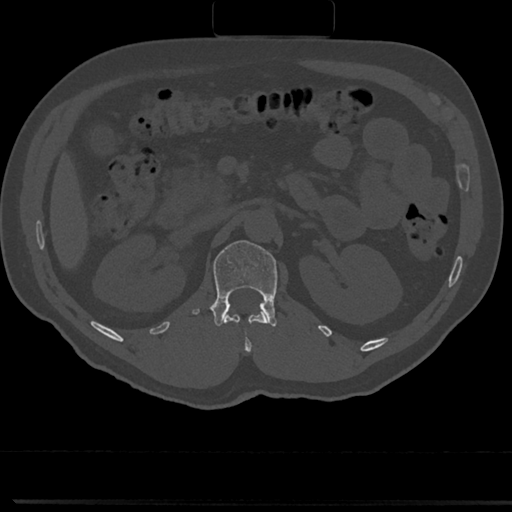
CT including the spine, one axial slice; position 100 of 817 along the scan axis; reconstruction kernel Br40s/3; 120 kVp; bone window (W 1800 / L 400 HU); 0.5 mm slice thickness; 512 × 512 image matrix, field of view 355 × 355 mm. Male patient, age 61 years. From the clinical record (not read from this slice): primary cancer: prostate.
Outlined on this slice (semi-automatic segmentation, software-assisted and operator-edited):
- L1 vertebra: bounding box (x1, y1, x2, y2) in pixels: (191, 240, 278, 327)
- T12 vertebra: (234, 313, 267, 350)